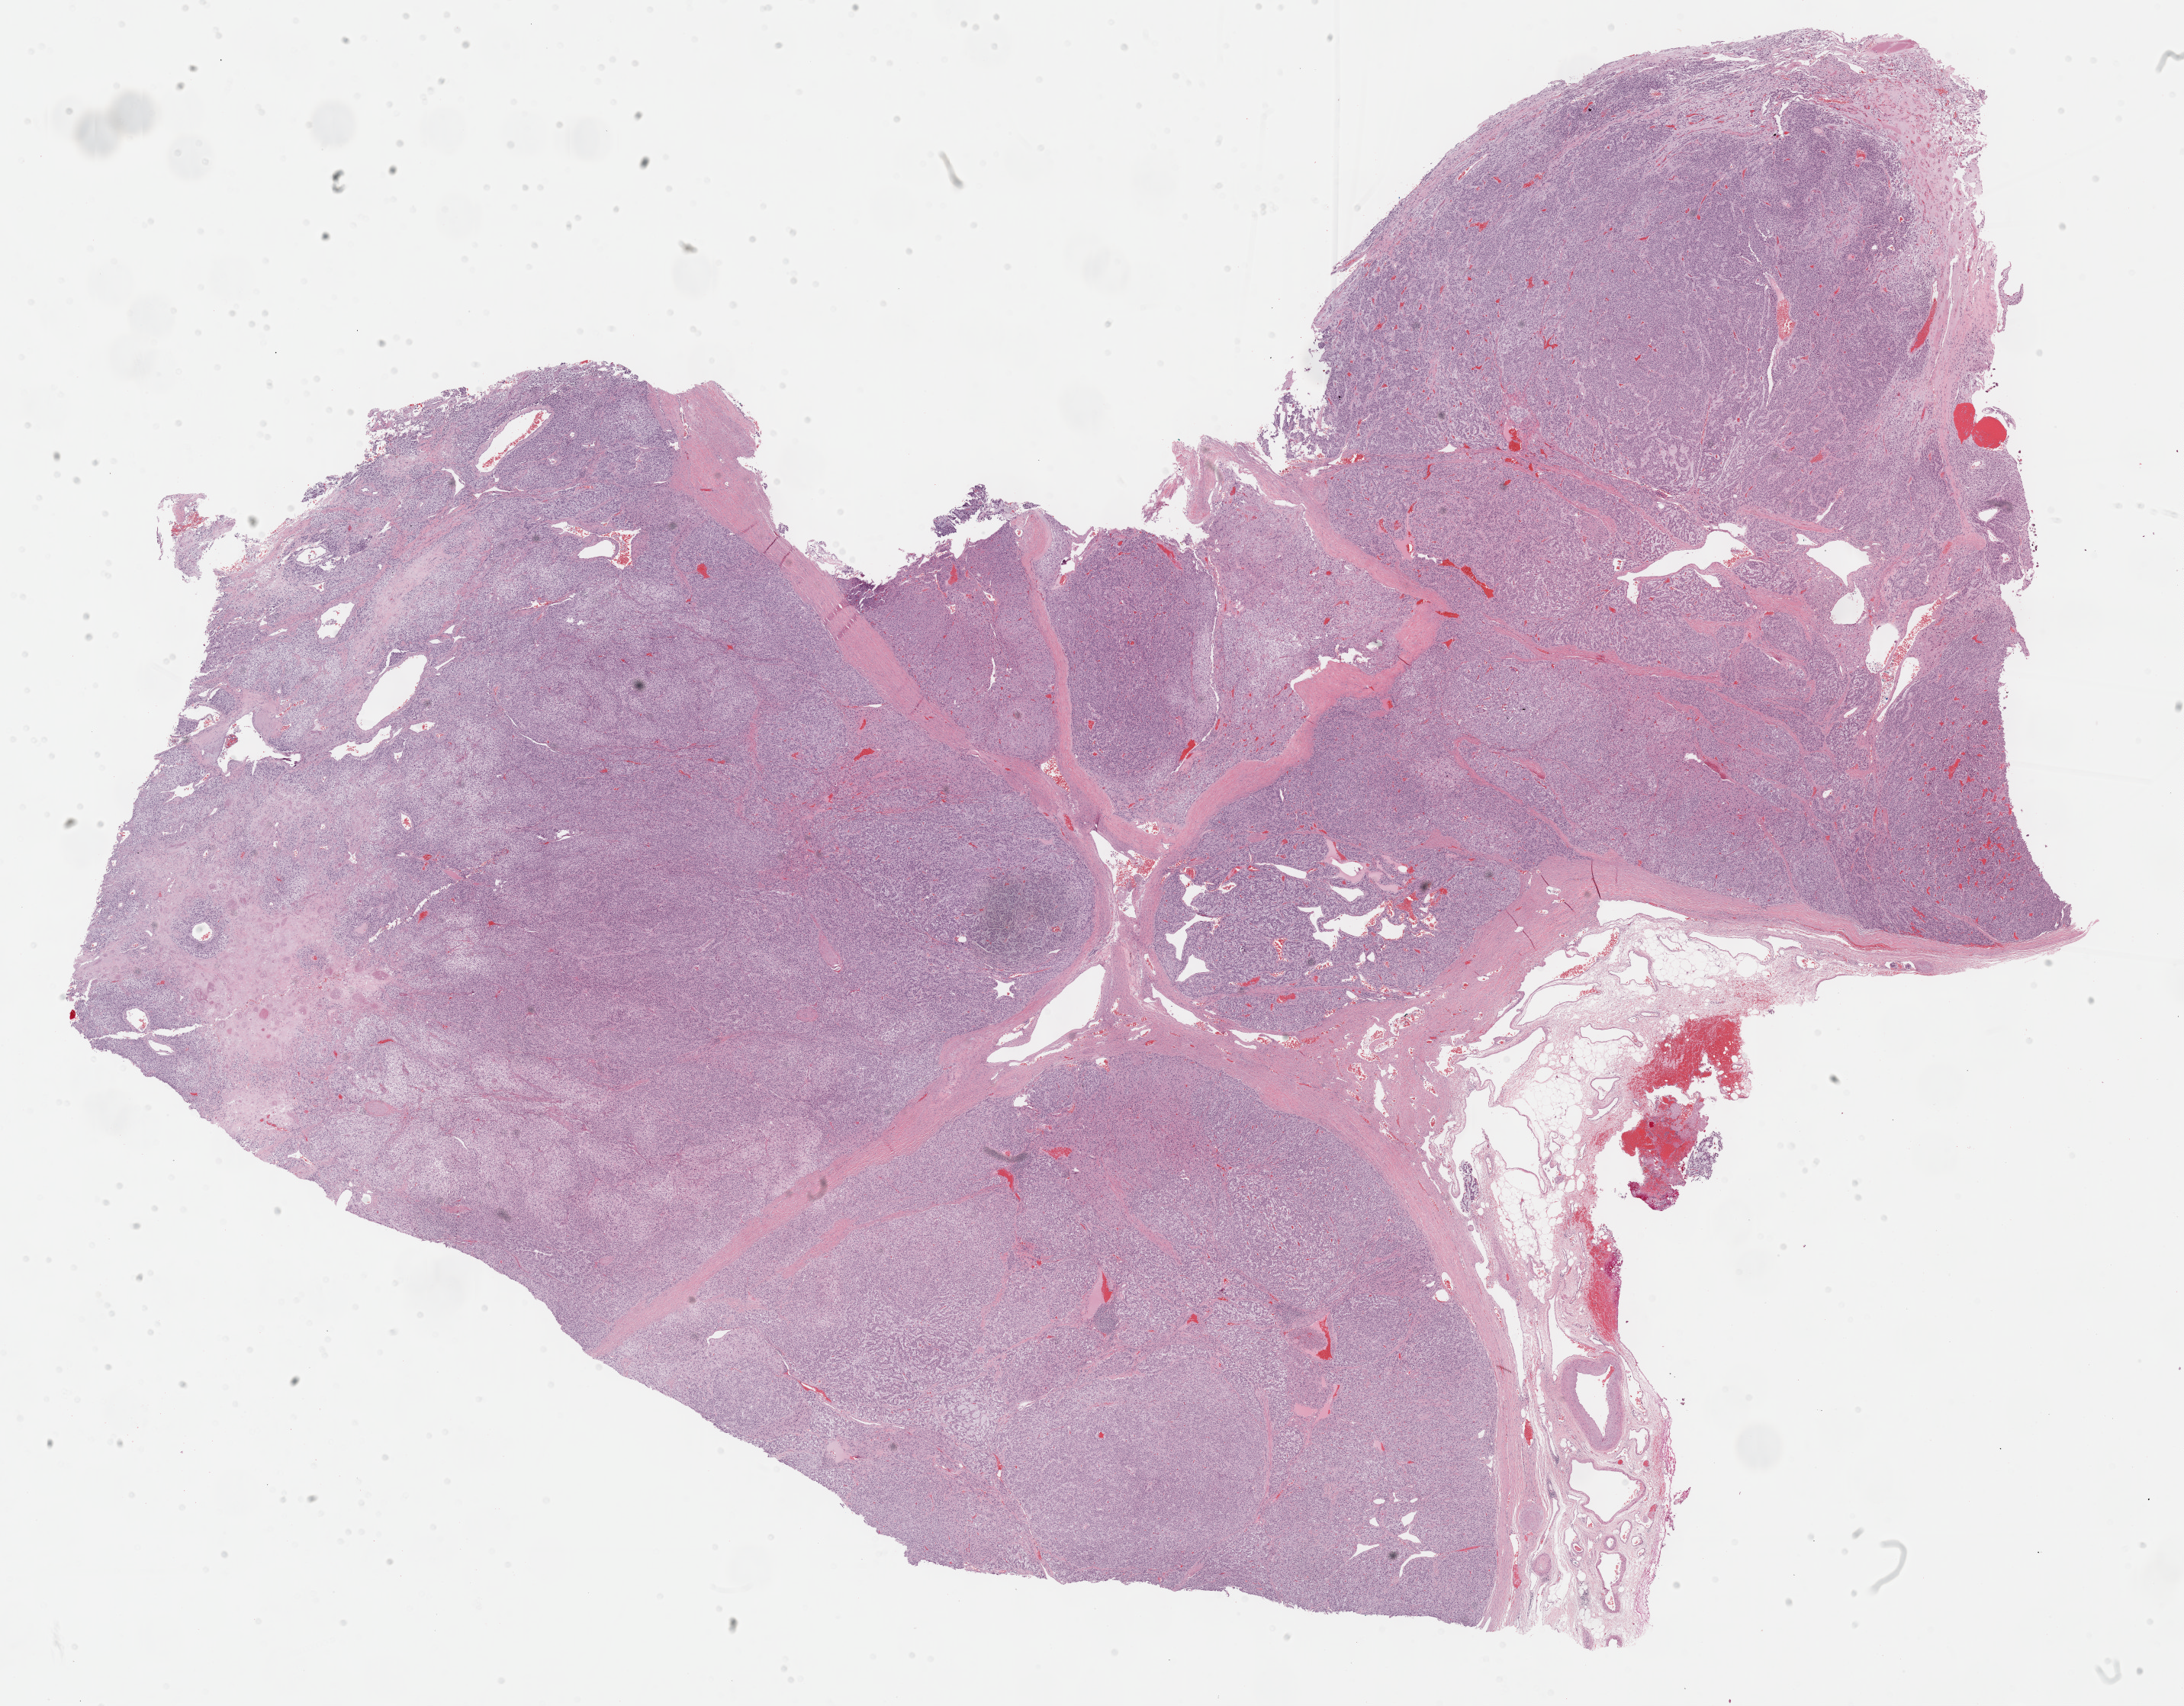
Whole-slide histology image, H&E — whole scanned area (about 23.2 x 18.1 mm) shown as a low-resolution overview, formalin-fixed paraffin-embedded (FFPE) diagnostic section, adrenal cortex, primary tumour sample. Male patient; age at initial diagnosis 50 years.
* lymph nodes positive (case pathology): 0 of 1 examined
* diagnosis: Adrenal cortical carcinoma (cortex of adrenal gland)